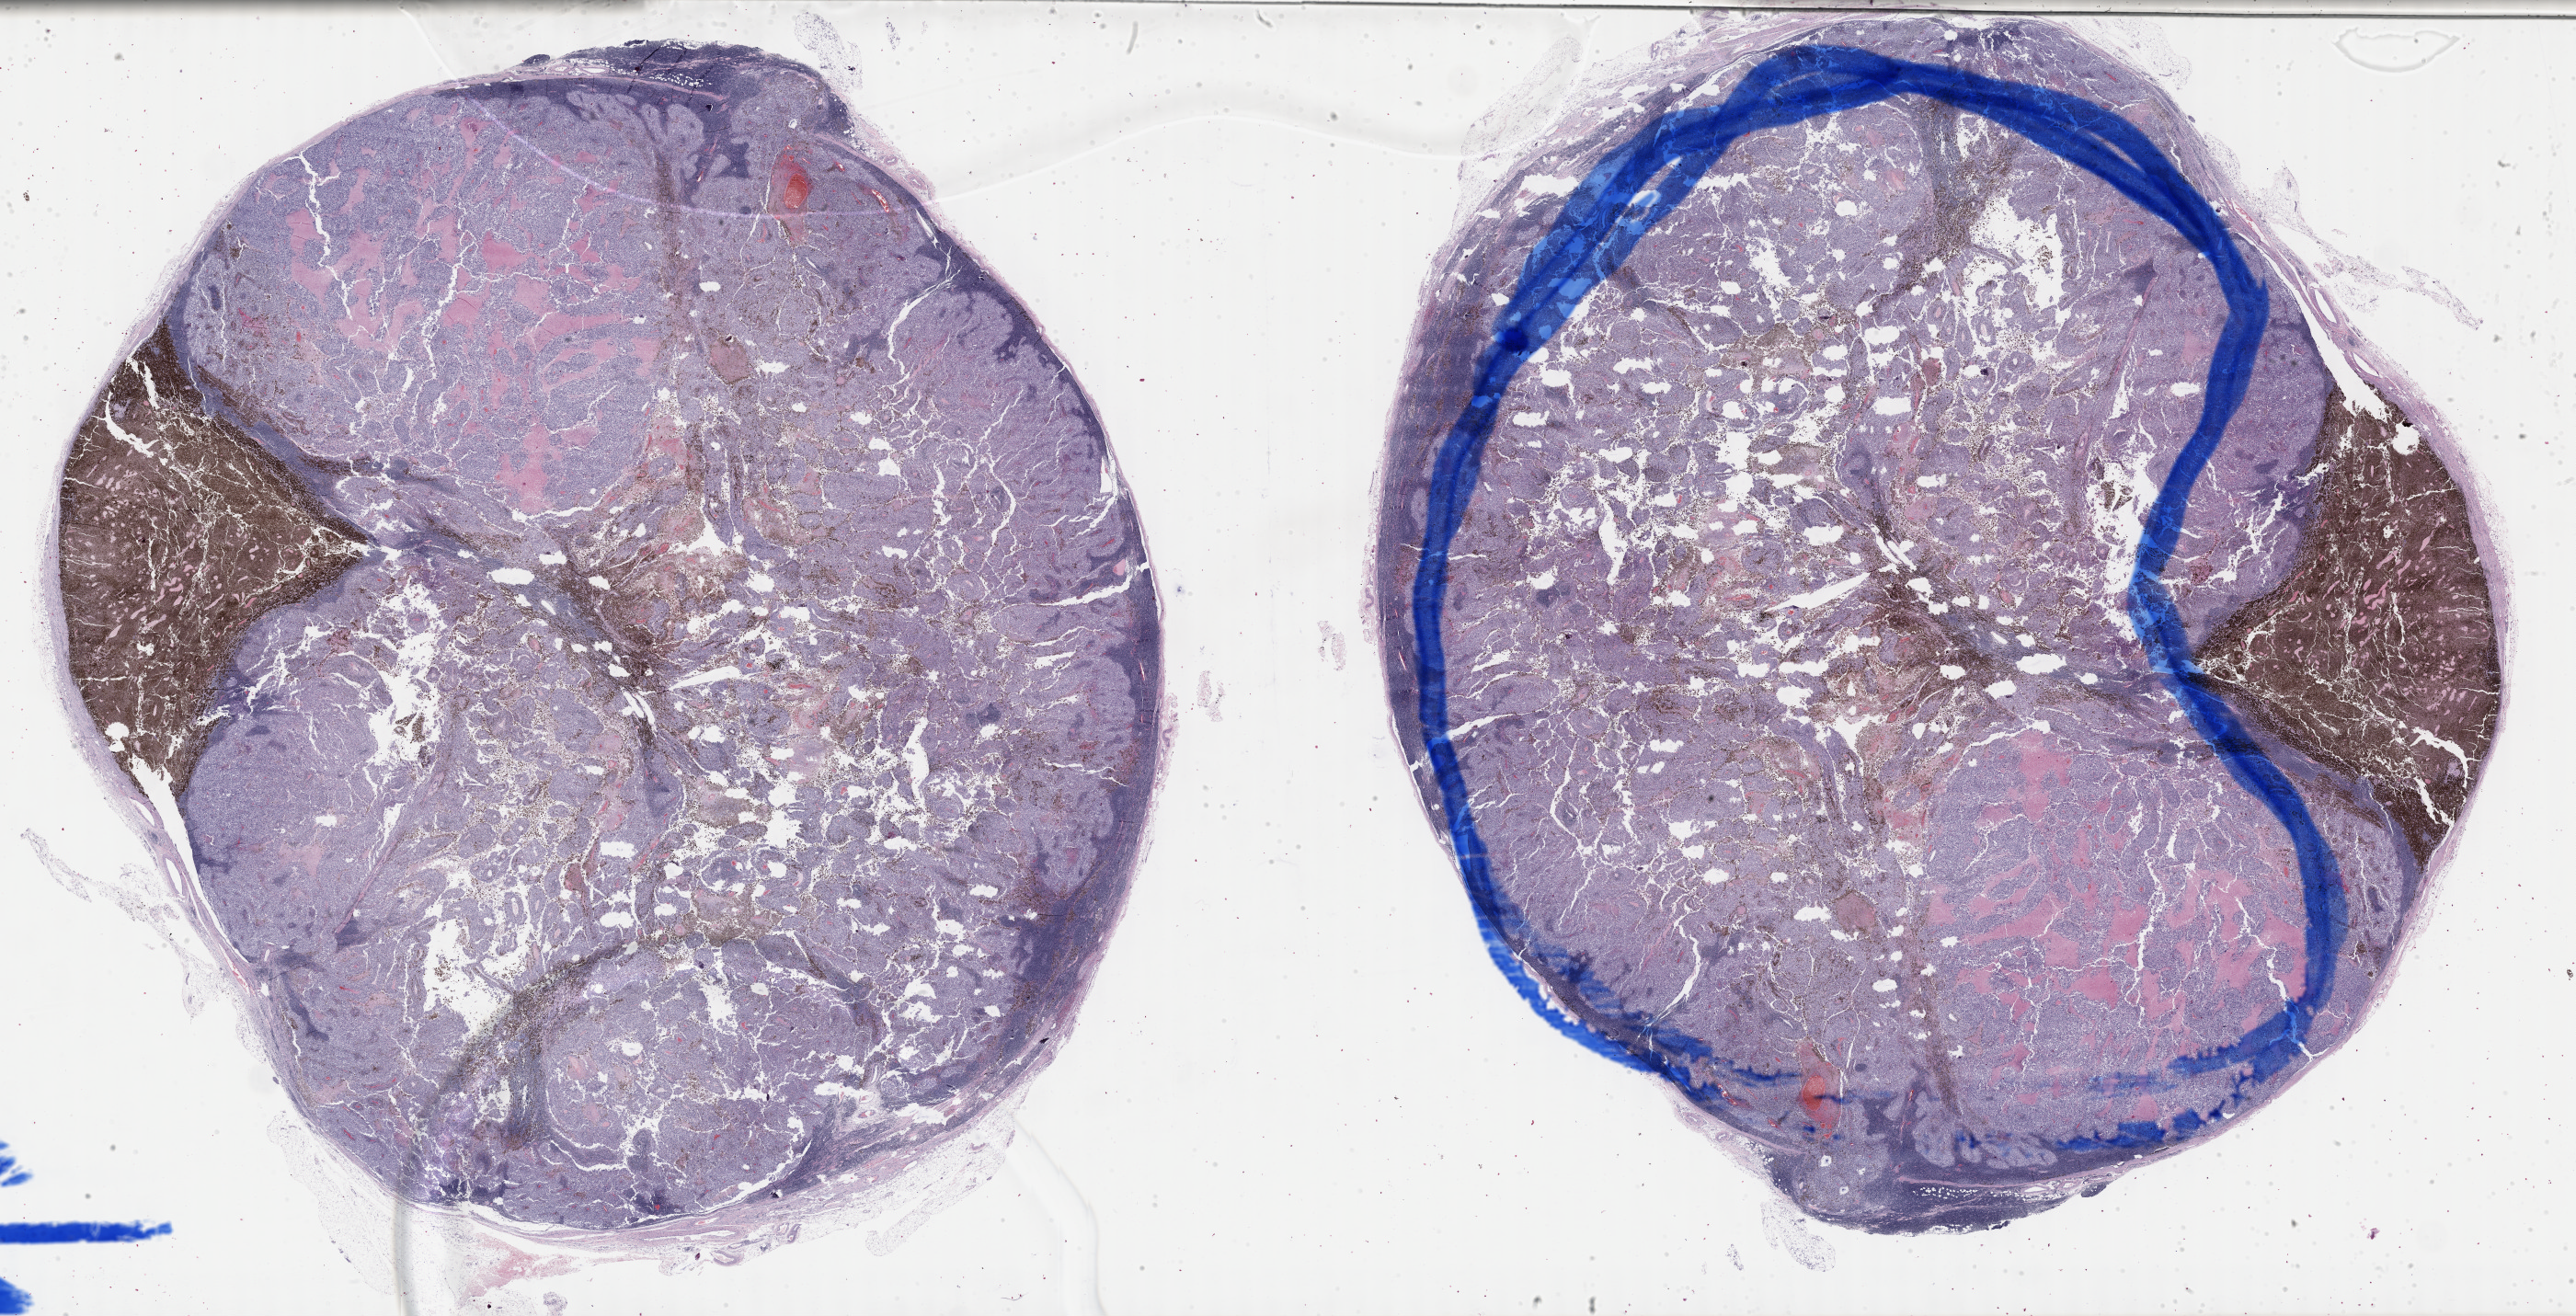
Whole-slide histology image, H&E — shown as a low-resolution overview of the whole scanned area (about 45.3 x 23.1 mm, acquisition: 40x scan), formalin-fixed paraffin-embedded (FFPE) diagnostic section, sample: primary tumour, skin. Patient: female, age at initial diagnosis 57 years.
• pathologic diagnosis: Malignant melanoma, NOS